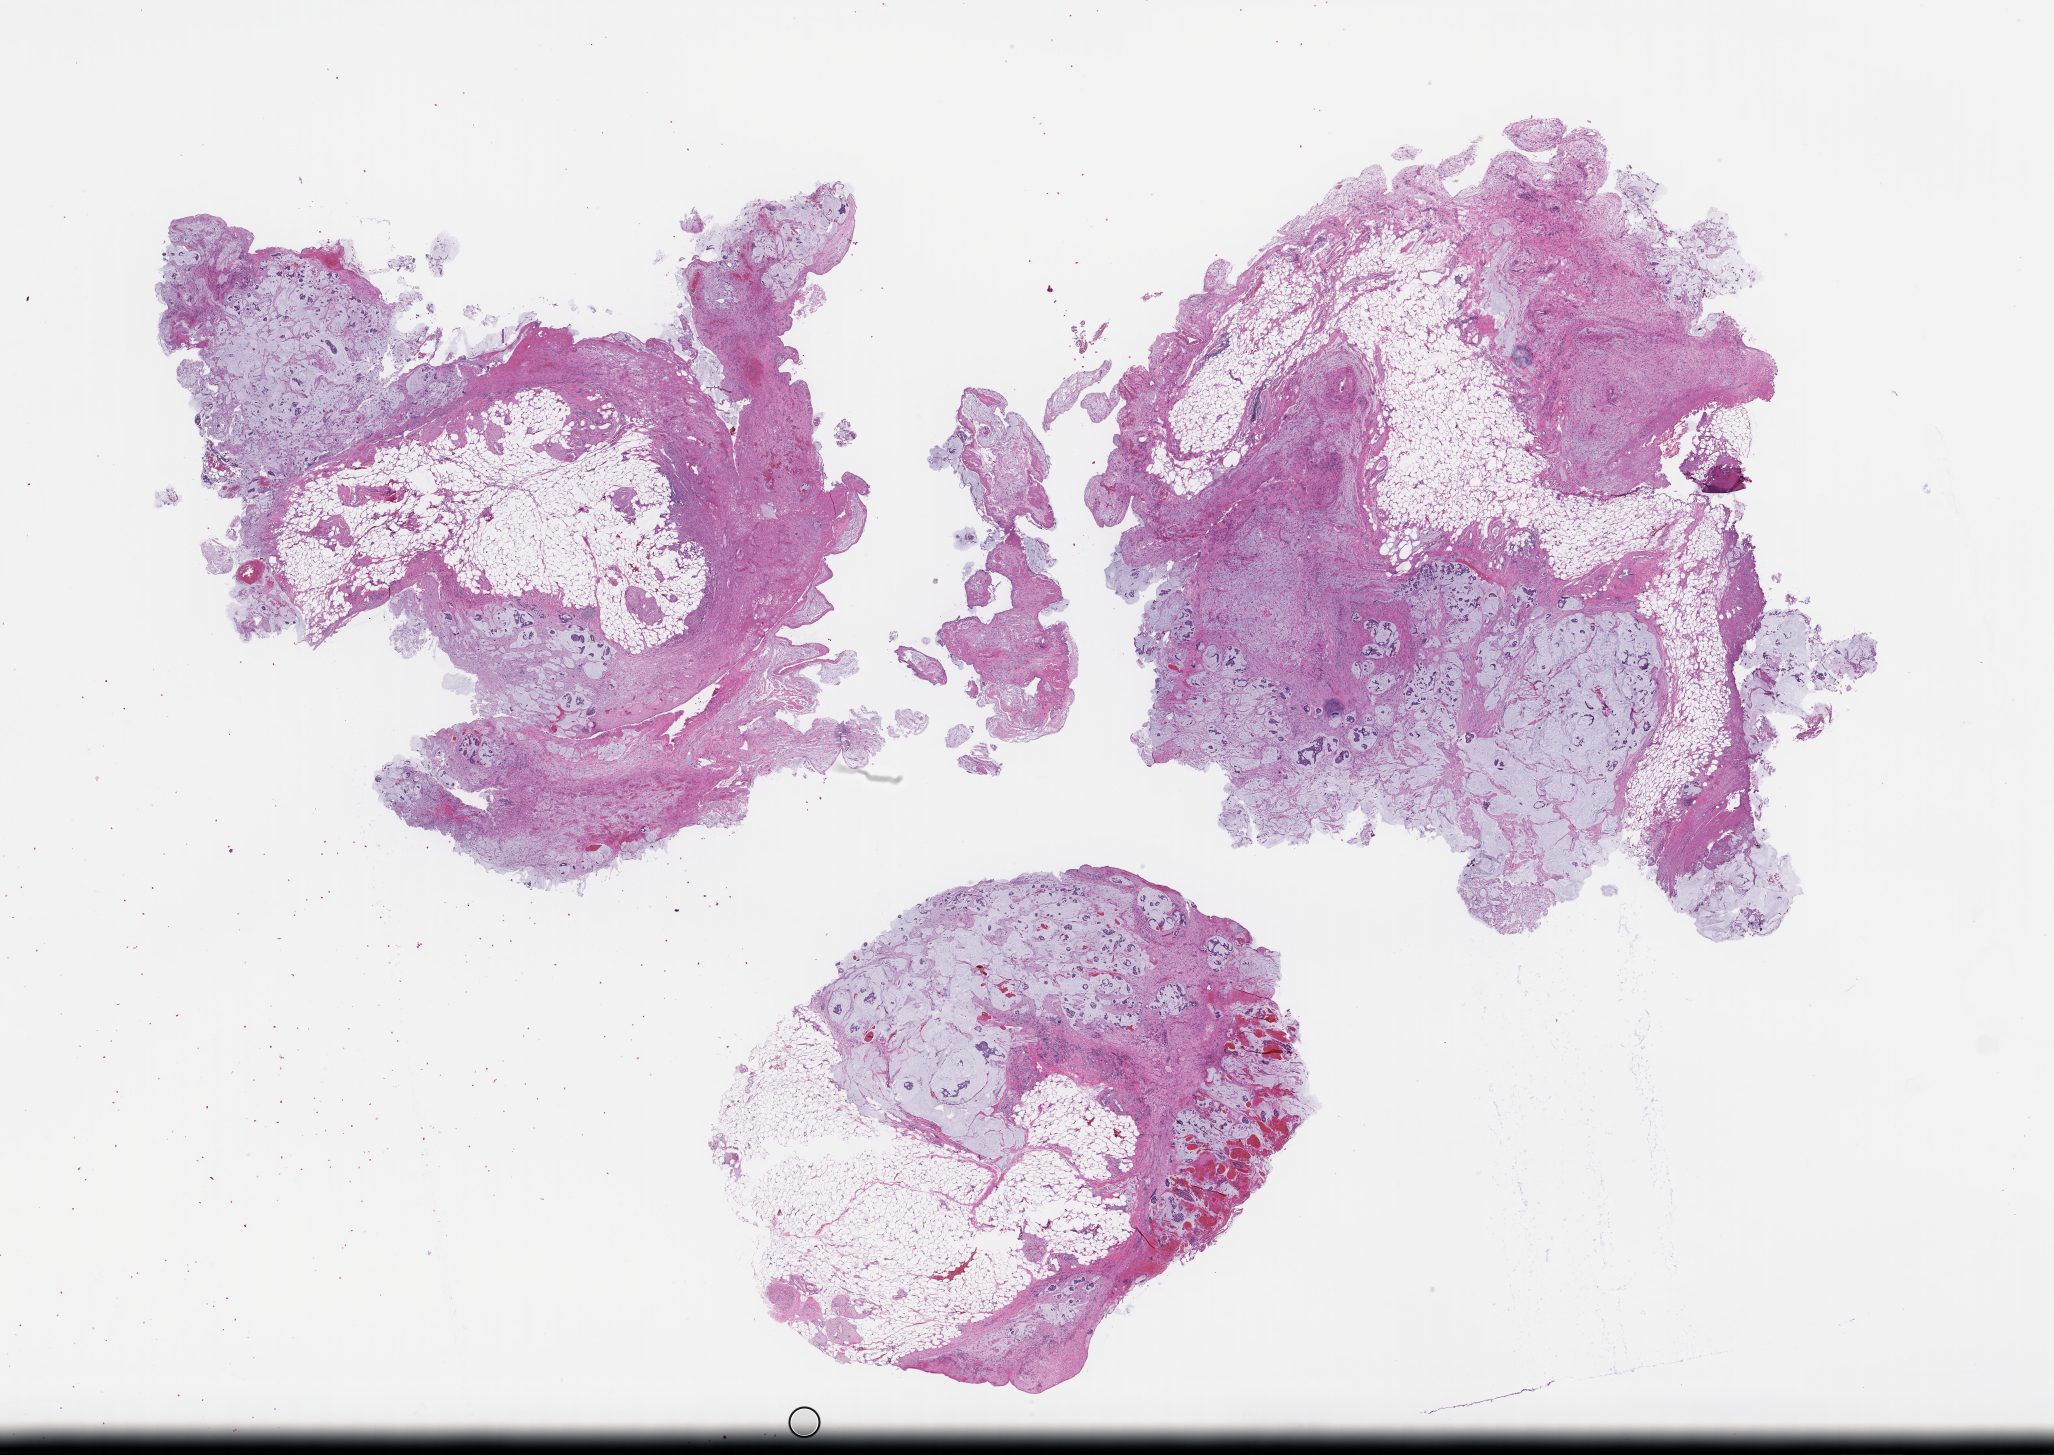
Whole-slide image, haematoxylin and eosin stain, a low-resolution overview of the entire scanned area, about 33.2 x 23.5 mm; FFPE section; tissue site: colon; specimen time point: collected at disease progression. Patient sex: male.
Patient diagnosis: Colorectal Carcinoma.